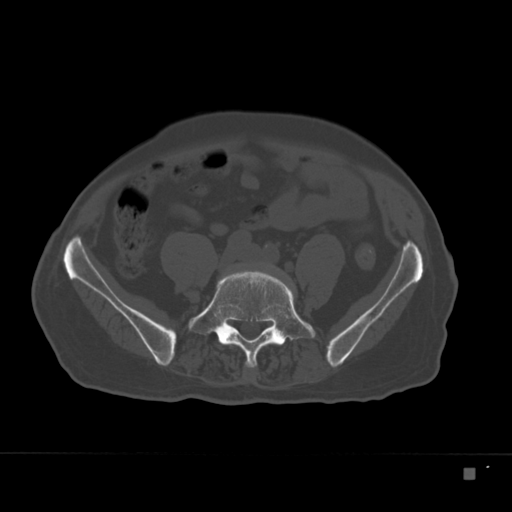
CT including the spine, one axial slice. Position 25 of 332 along the scan axis. Reconstruction kernel Br40s. Bone window (W 1800 / L 400 HU). 1.5 mm slice thickness. 512 × 512 image matrix, field of view 389 × 389 mm. Patient: male, 72 years. From the clinical record (not read from this slice): primary cancer: skeletal.
Annotated regions visible in this slice (semi-automatically segmented with operator editing):
- L5 vertebra: bounding box [x1, y1, x2, y2] px = [192, 271, 316, 367]